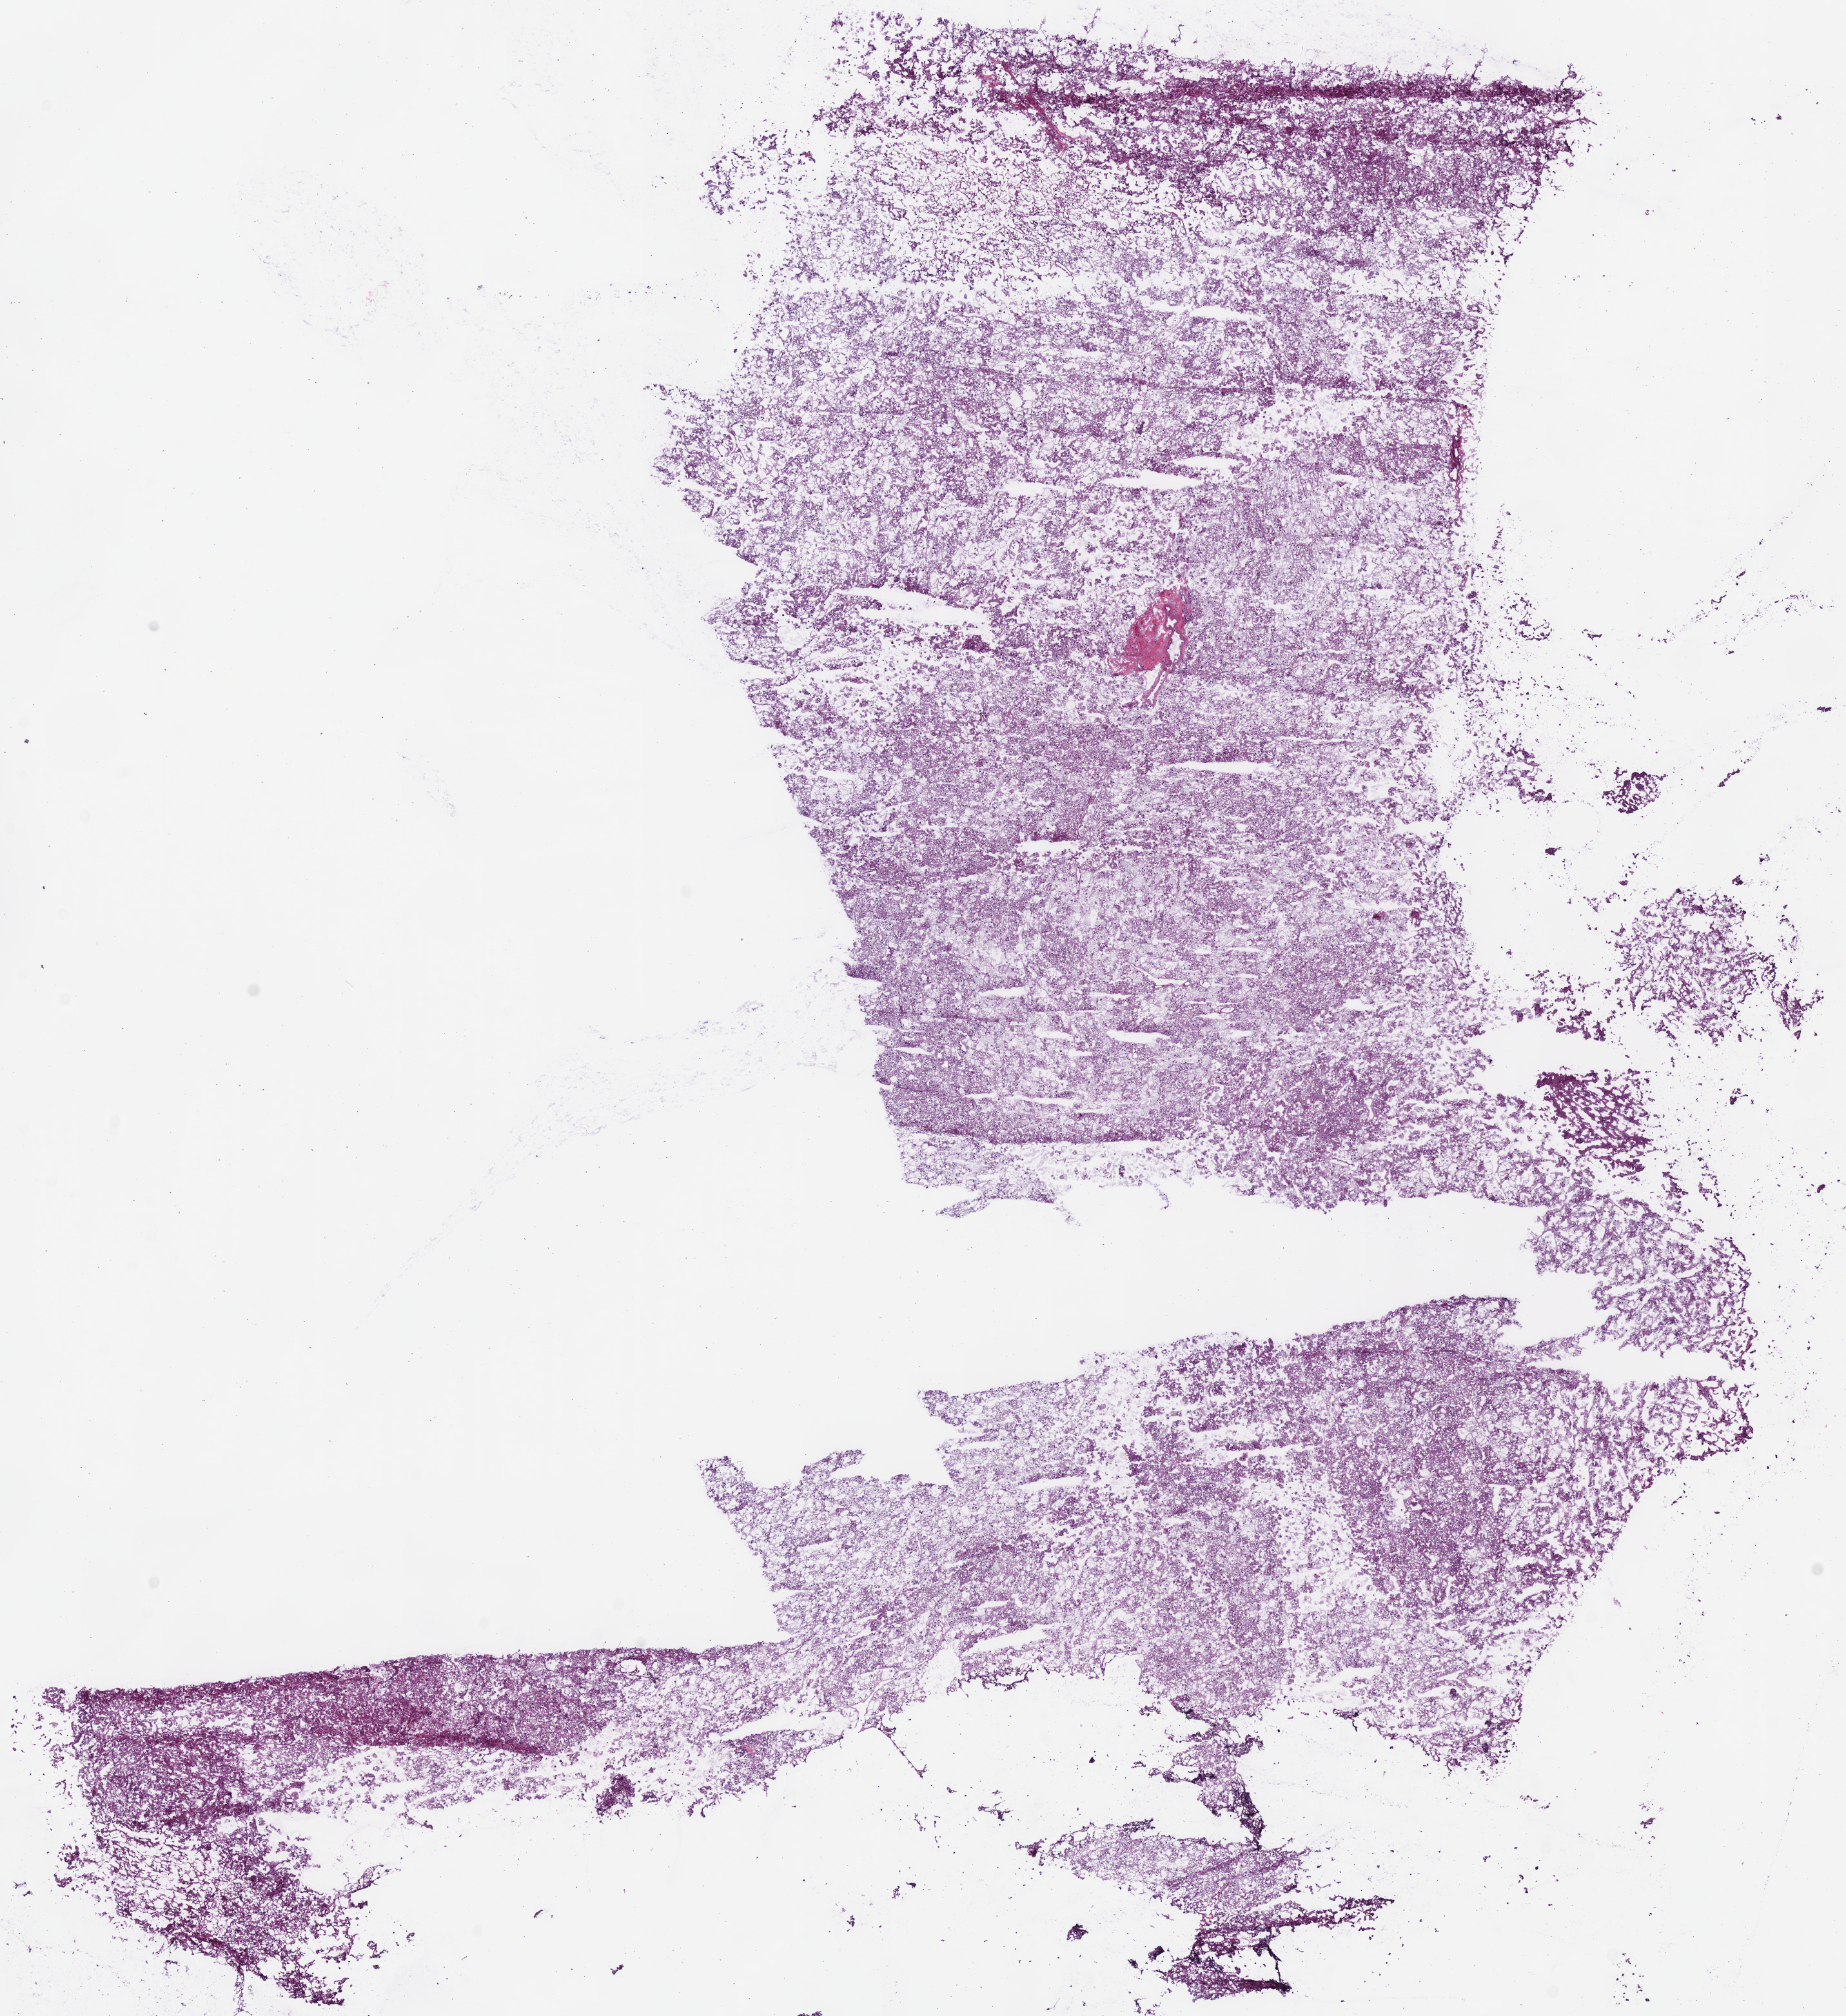
Whole-slide histology image, Hematoxylin and eosin (H&E) stained, a low-resolution overview of the entire scanned area, about 11.3 x 12.3 mm (acquisition: 40x scan); frozen section; primary tumour sample from the kidney. Female, age 17 years at initial diagnosis. Slide review estimates, as recorded: tumour cells 90%, tumour nuclei 90%, normal cells 0%, stromal cells 10%, necrosis 0%.
- AJCC pathologic stage: I
- pathologic diagnosis: Renal cell carcinoma, chromophobe type